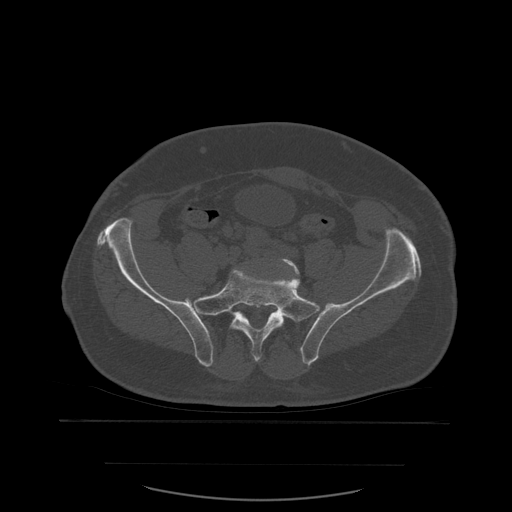
CT including the spine, one axial slice; position 117 of 590 along the scan axis; bone window (W 1800 / L 400 HU); 512 × 512 image matrix, field of view 479 × 479 mm. Patient age 71 years. From the clinical record (not read from this slice): primary cancer: lung; vertebrae with lytic lesions (as recorded): T1, T2, L5, S1.
Annotated regions visible in this slice (semi-automatic segmentation, software-assisted and operator-edited):
- L5 vertebra: bounding box (x1, y1, x2, y2) in pixels: (253, 259, 300, 357)